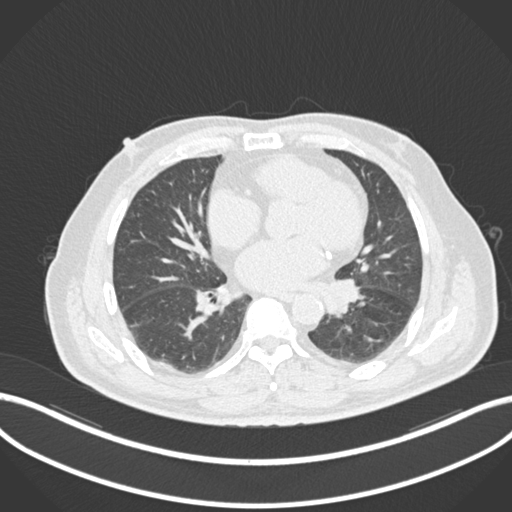
Chest CT, one axial slice; slice 57 of 161 in the series (ordered by position); lung window (W 1500 / L -600 HU); 1 mm slice thickness; 512 × 512 image matrix, field of view 400 × 400 mm. Male patient, age 71 years. From the clinical record (not read from this slice): clinical TNM (as recorded): T1b N0 M0.
Outlined on this slice (bounding box drawn by a radiologist):
- lung tumour (recorded histology: squamous cell carcinoma): bounding box (x1, y1, x2, y2) in pixels: (323, 274, 360, 319)